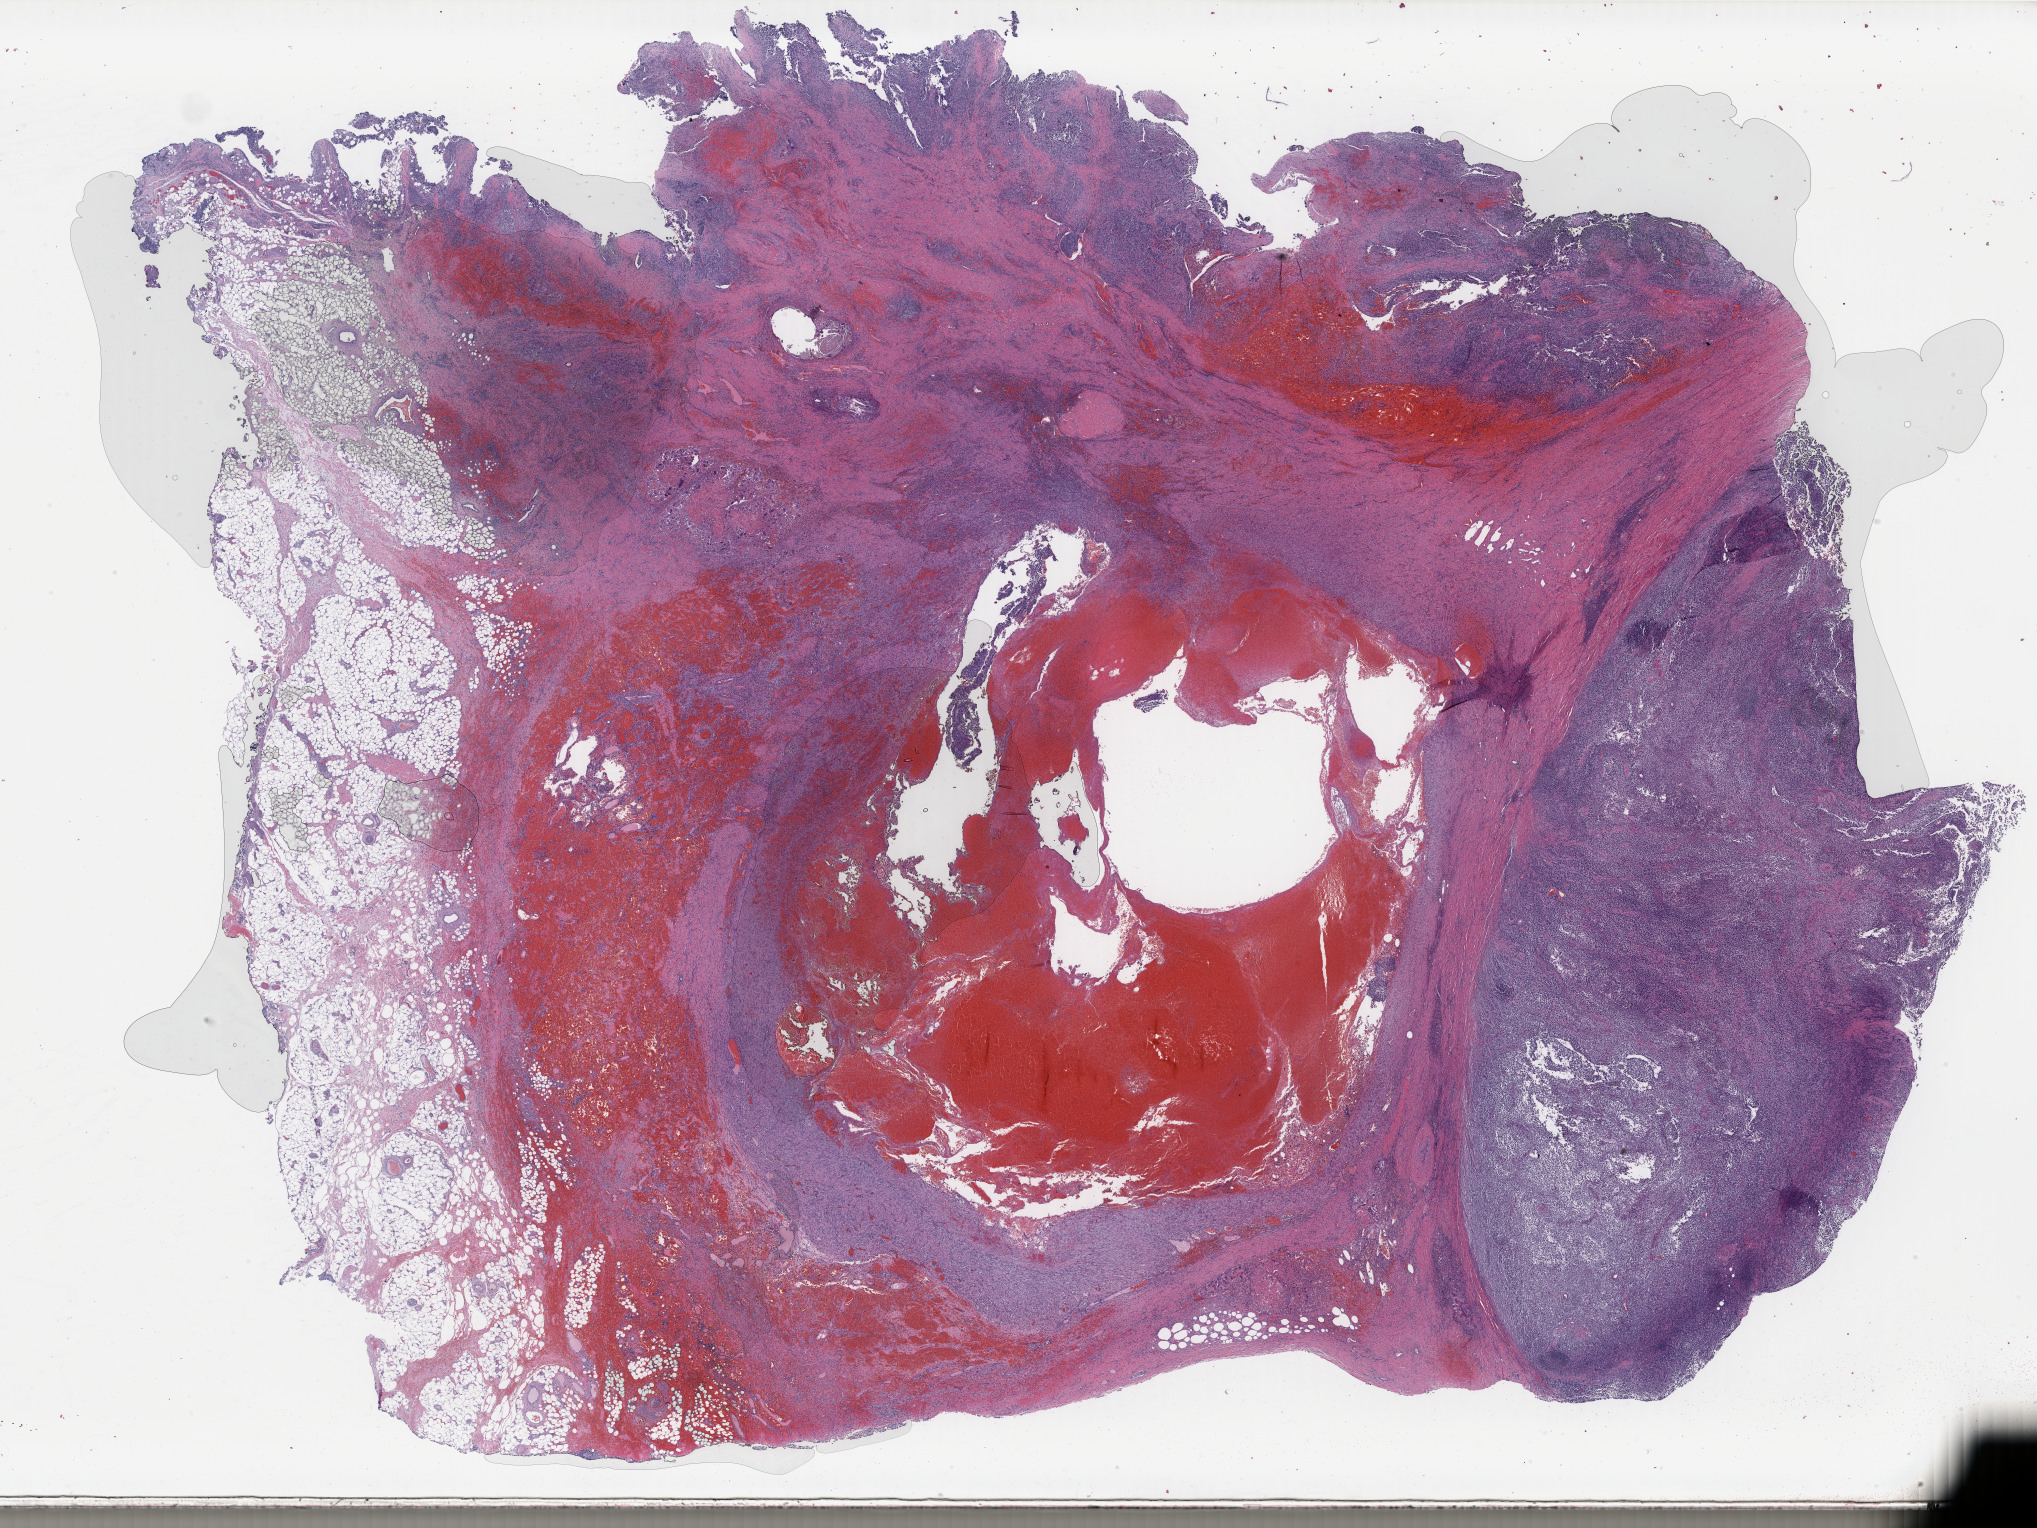
Digitized H&E tissue section (whole slide), shown as a low-resolution overview of the whole scanned area (about 32.3 x 24.3 mm). FFPE section. Primary tumour sample from the skin. Female patient; age at initial diagnosis 46 years.
Histologic diagnosis: Malignant melanoma, NOS.